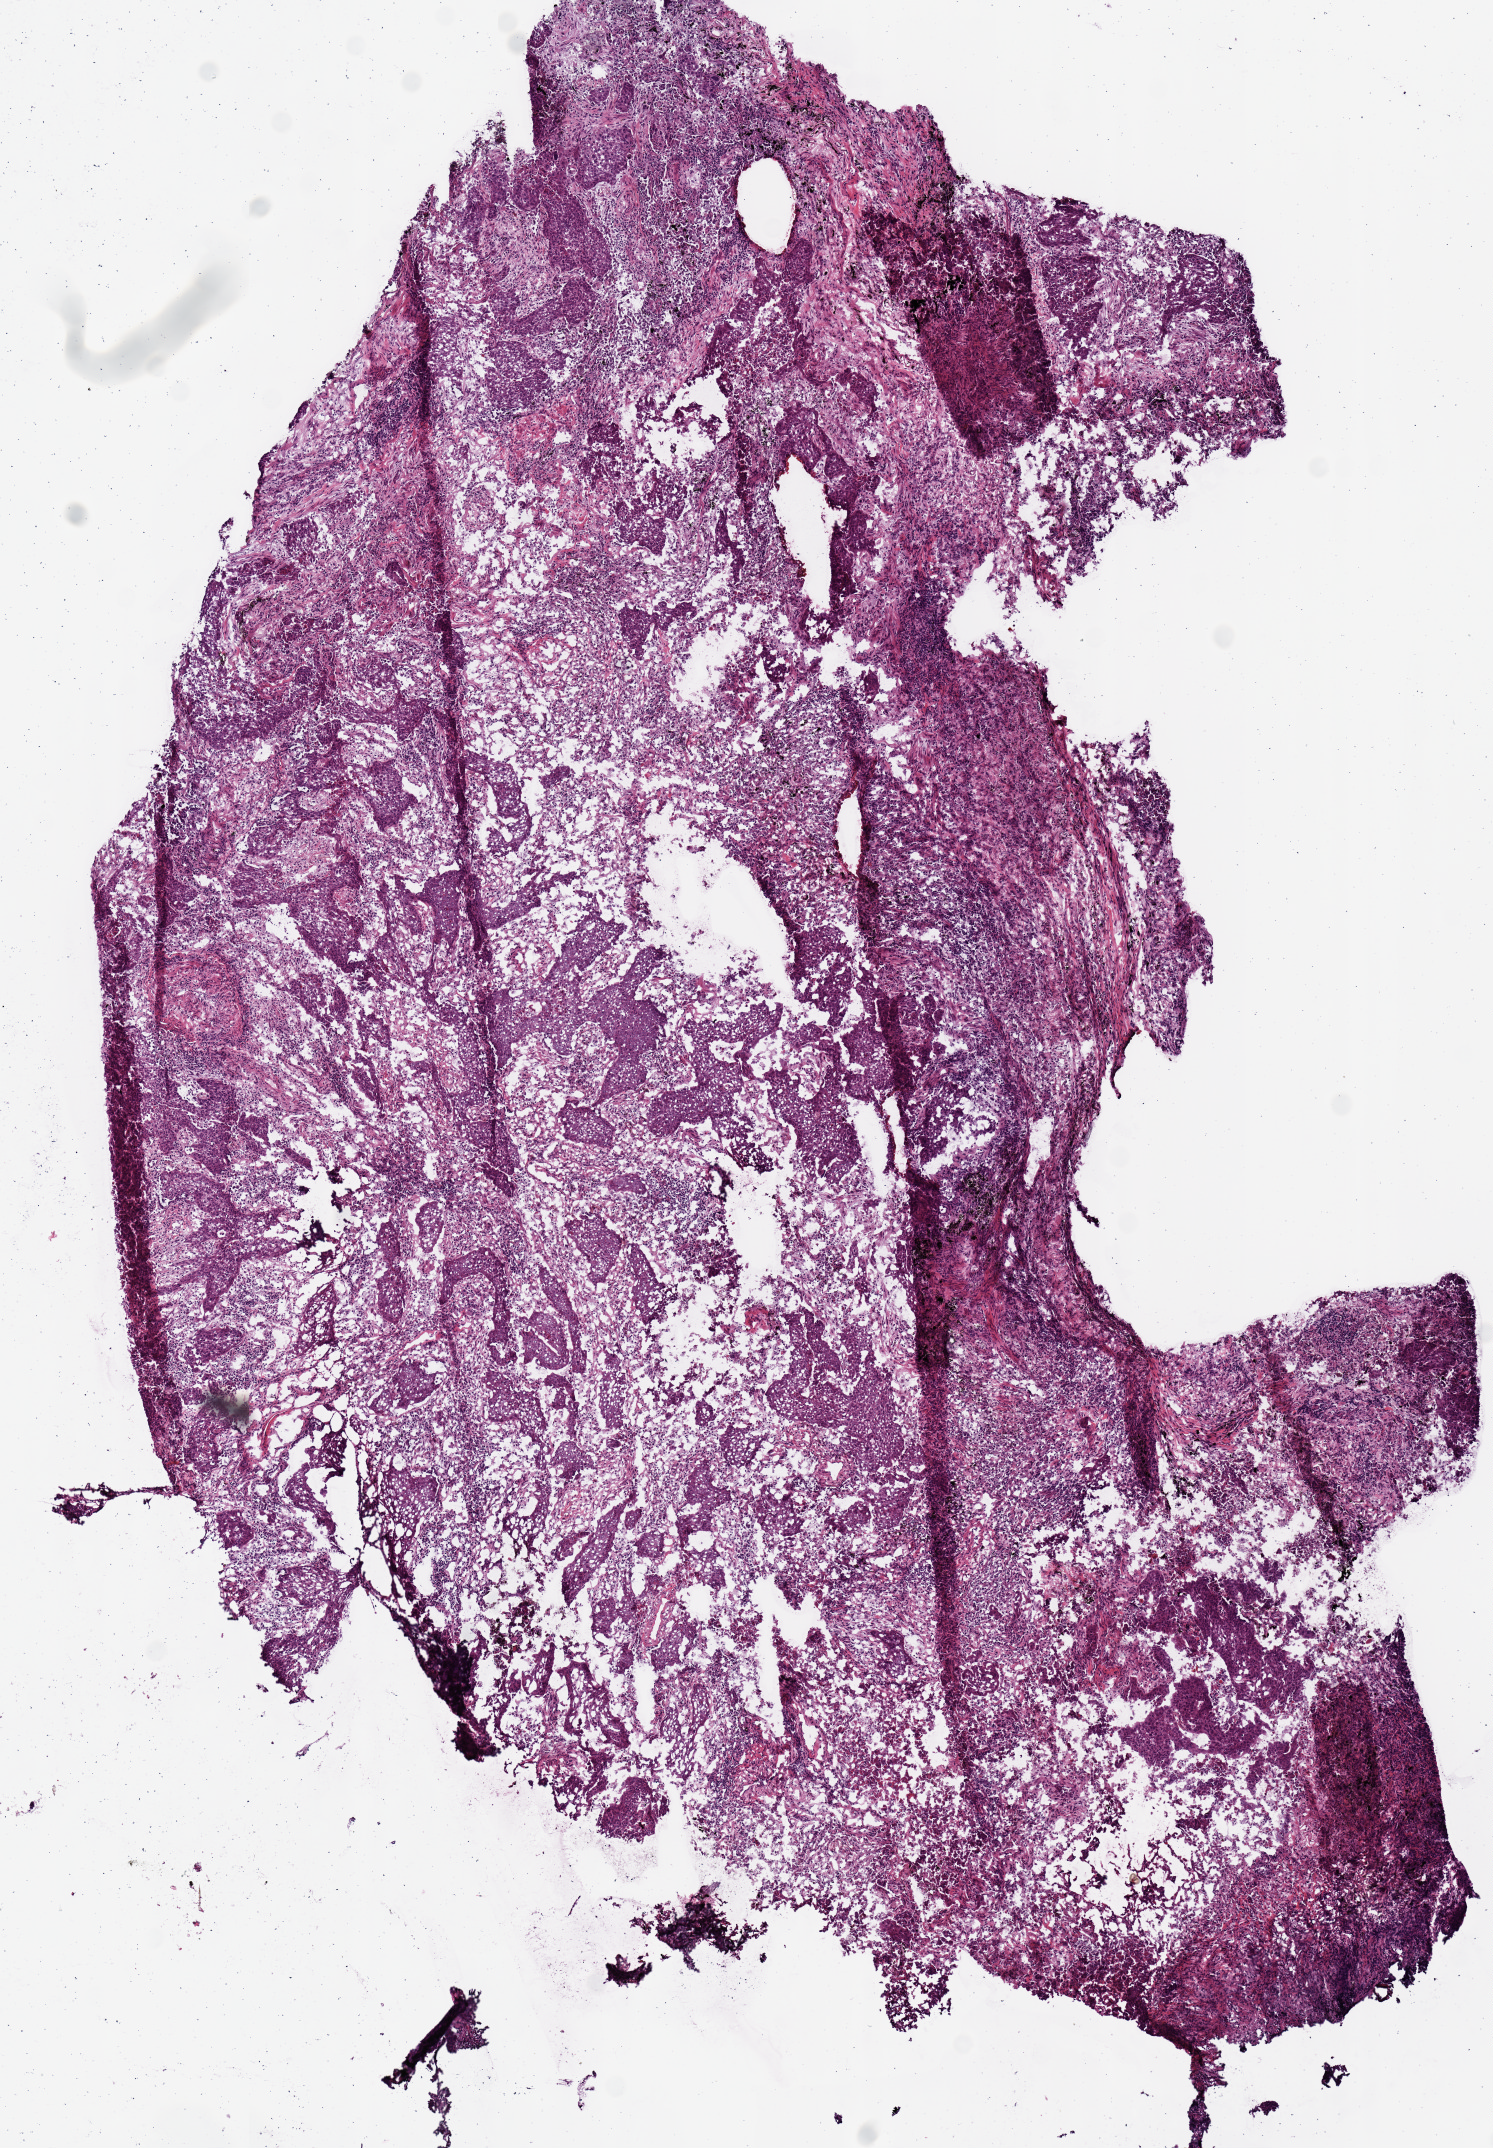
Digitized H&E-stained tissue section (whole slide), shown as a low-resolution overview of the whole scanned area (about 5.9 x 8.5 mm, slide scanned at 20x). Frozen section from the top of the tissue portion. Primary tumour sample from the lung. Female patient; age at initial diagnosis 66 years. Slide review estimates, as recorded: tumour cells 80%, tumour nuclei 60%, normal cells 0%, stromal cells 20%, necrosis 0%.
TNM: T2 N1 M0. AJCC pathologic stage: IIB (6th edition). Diagnosis: Squamous cell carcinoma, NOS (lower lobe, lung). Laterality: right.